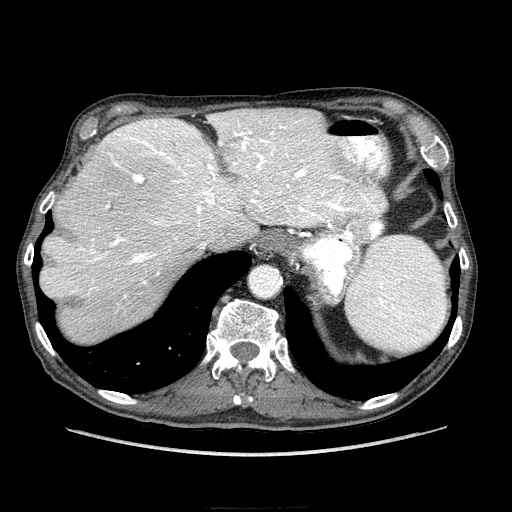
Contrast-enhanced abdominal CT (liver protocol), one axial slice. Position 175 of 218 along the scan axis. Reconstruction kernel STANDARD. 100 kVp. Soft-tissue window (W 400 / L 40 HU). 2.5 mm slice thickness. 512 × 512 image matrix, field of view 380 × 380 mm. From the clinical record (not read from this slice): diagnosis: hepatocellular carcinoma (patient treated with transarterial chemoembolisation; whether this scan precedes or follows treatment is not stated here); TNM stage (as recorded): Stage-IIIA; Child-Pugh class: A; tumour nodularity: multinodular; tumour size: 20 cm.
Structures marked on this image (semi-automatically segmented with operator editing):
- abdominal aorta: box from (x=249, y=267) to (x=280, y=296) px
- liver parenchyma outside the tumour (the mass and vessels are separate outlines, so this box may not span the whole liver): (x=40, y=108)–(x=386, y=344)
- liver vessels: (x=44, y=117)–(x=385, y=298)